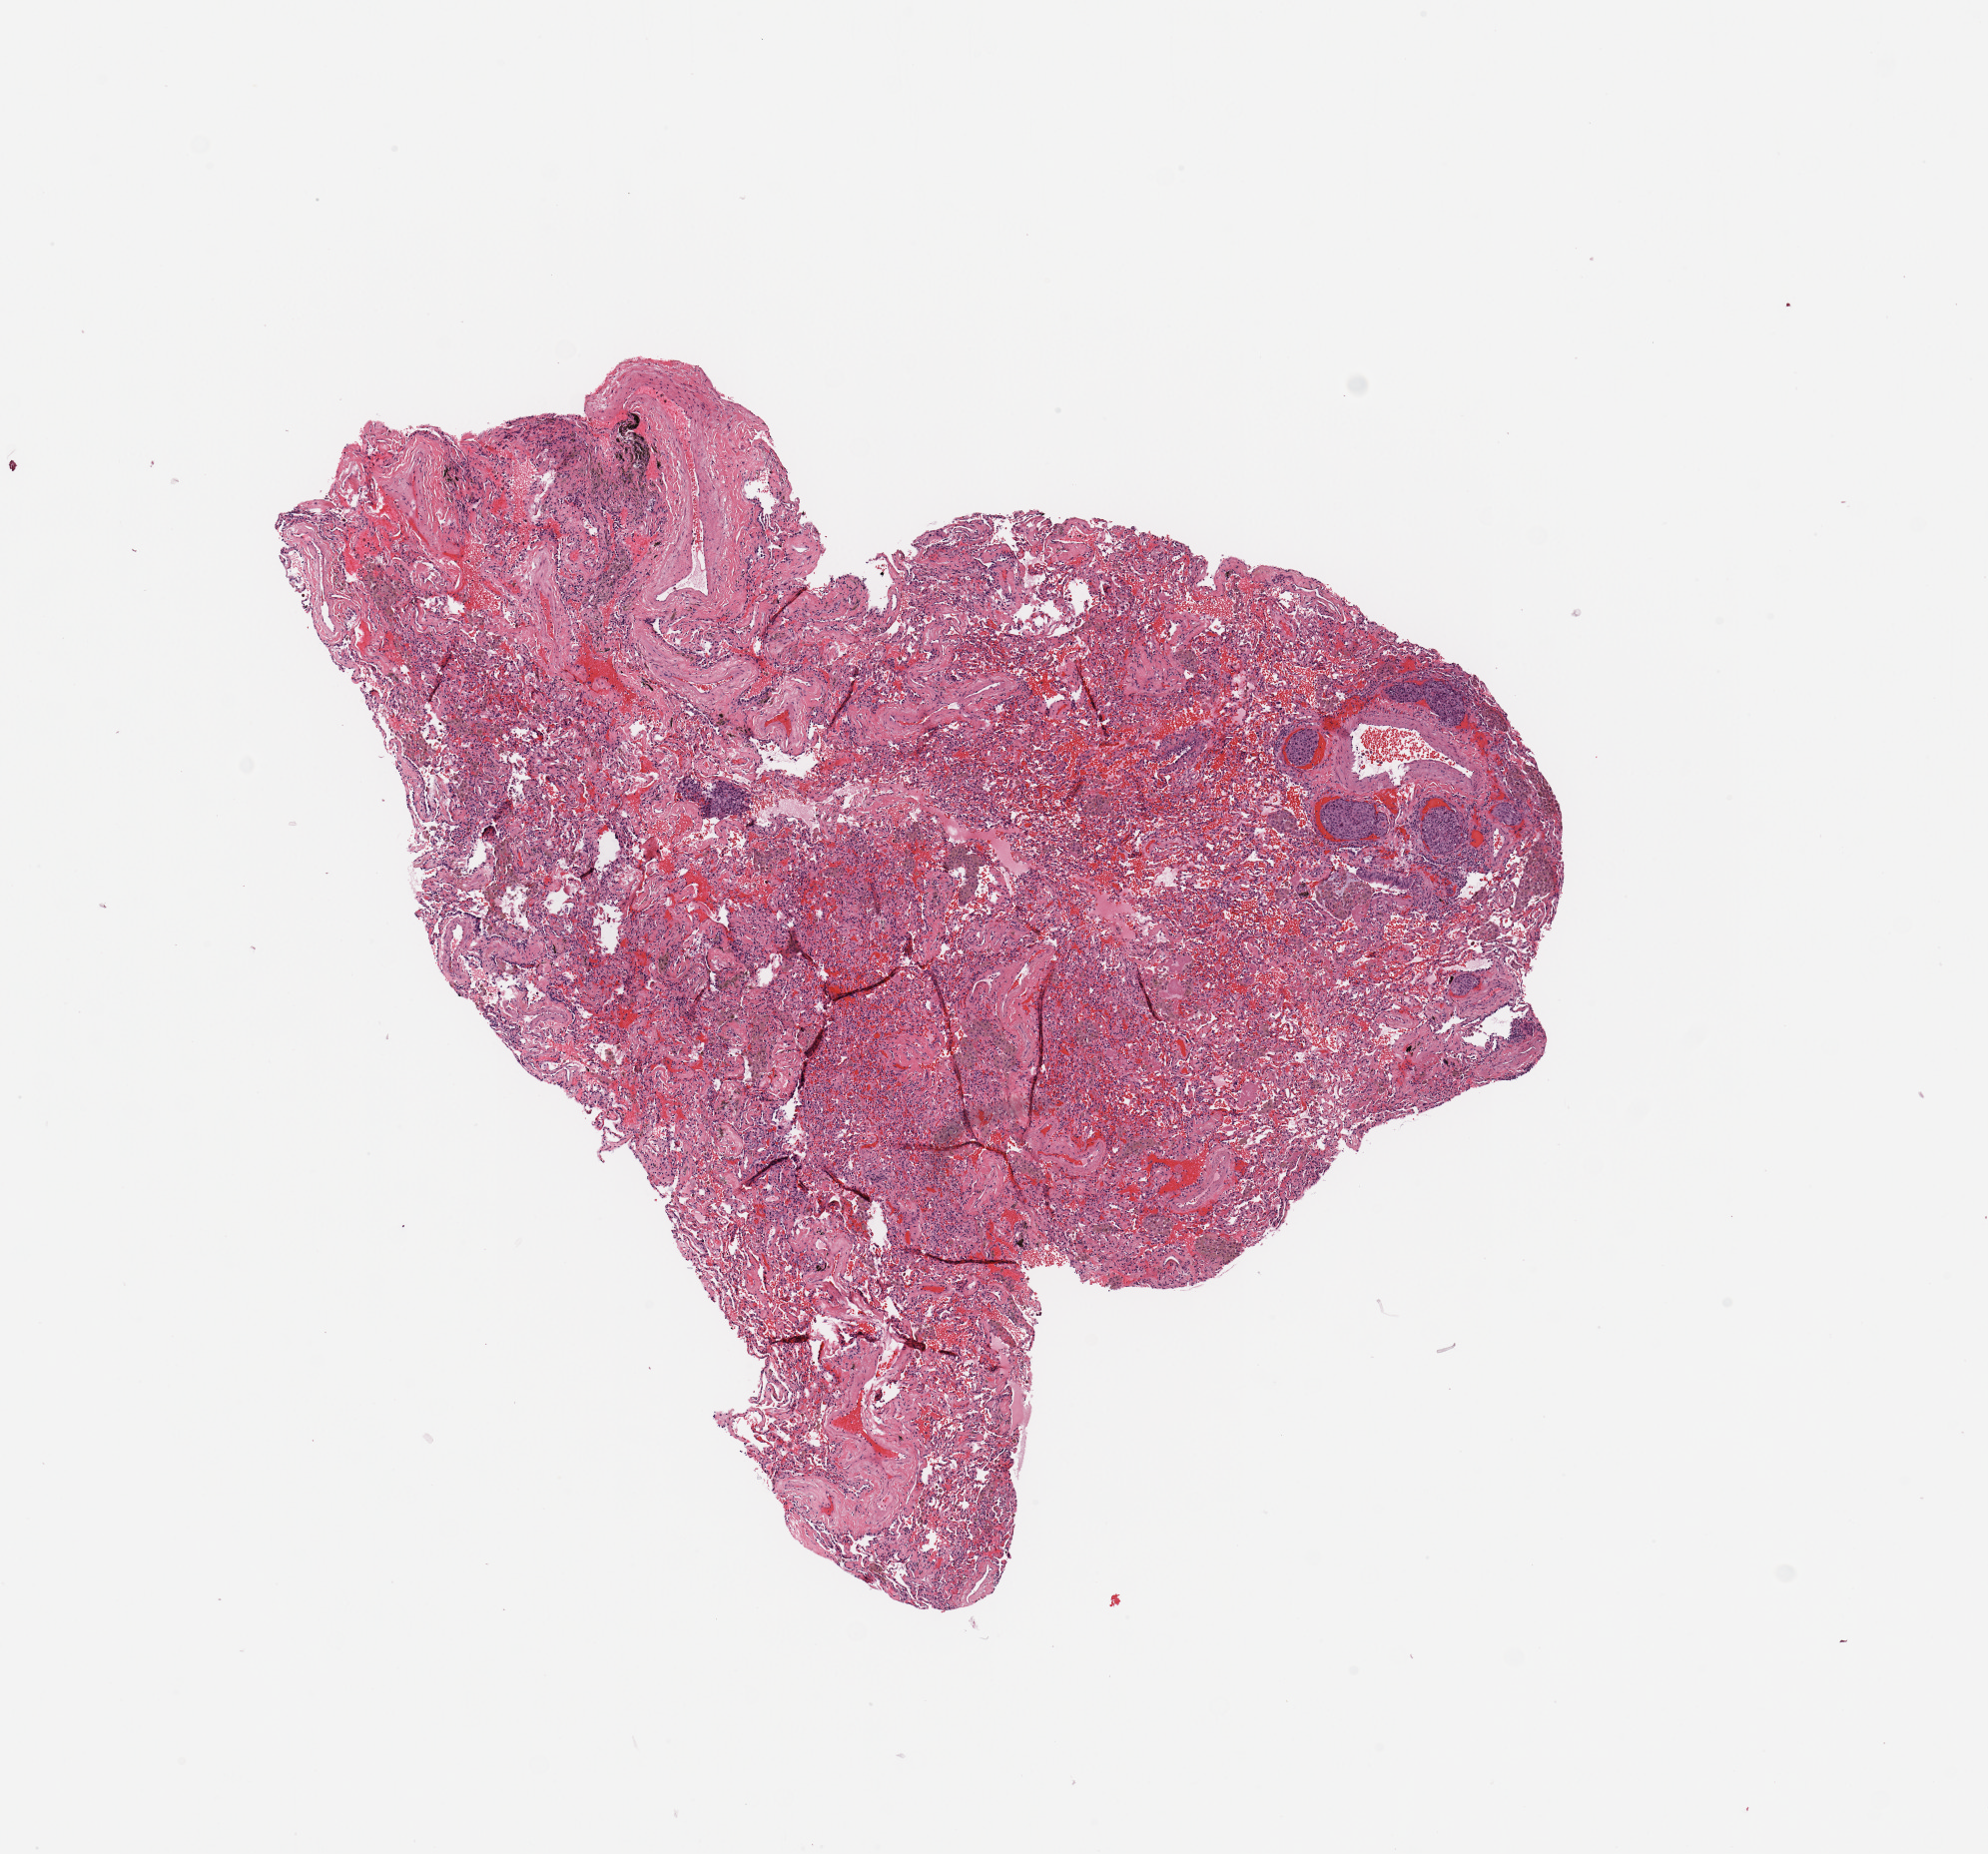
Whole-slide histology image, H&E — low-resolution overview of the scanned area, about 7.9 x 7.3 mm (acquisition: 20x scan); tumour tissue sample, sampled site: lung. Male, 49 y/o. Histologic grade: G3 (poorly differentiated). Slide review estimates, as recorded: tumour nuclei 80%, necrosis 3%.
- AJCC pathologic stage: IIIA
- diagnosis: Squamous cell carcinoma, NOS
- primary tumour site (as recorded): left lower lobe